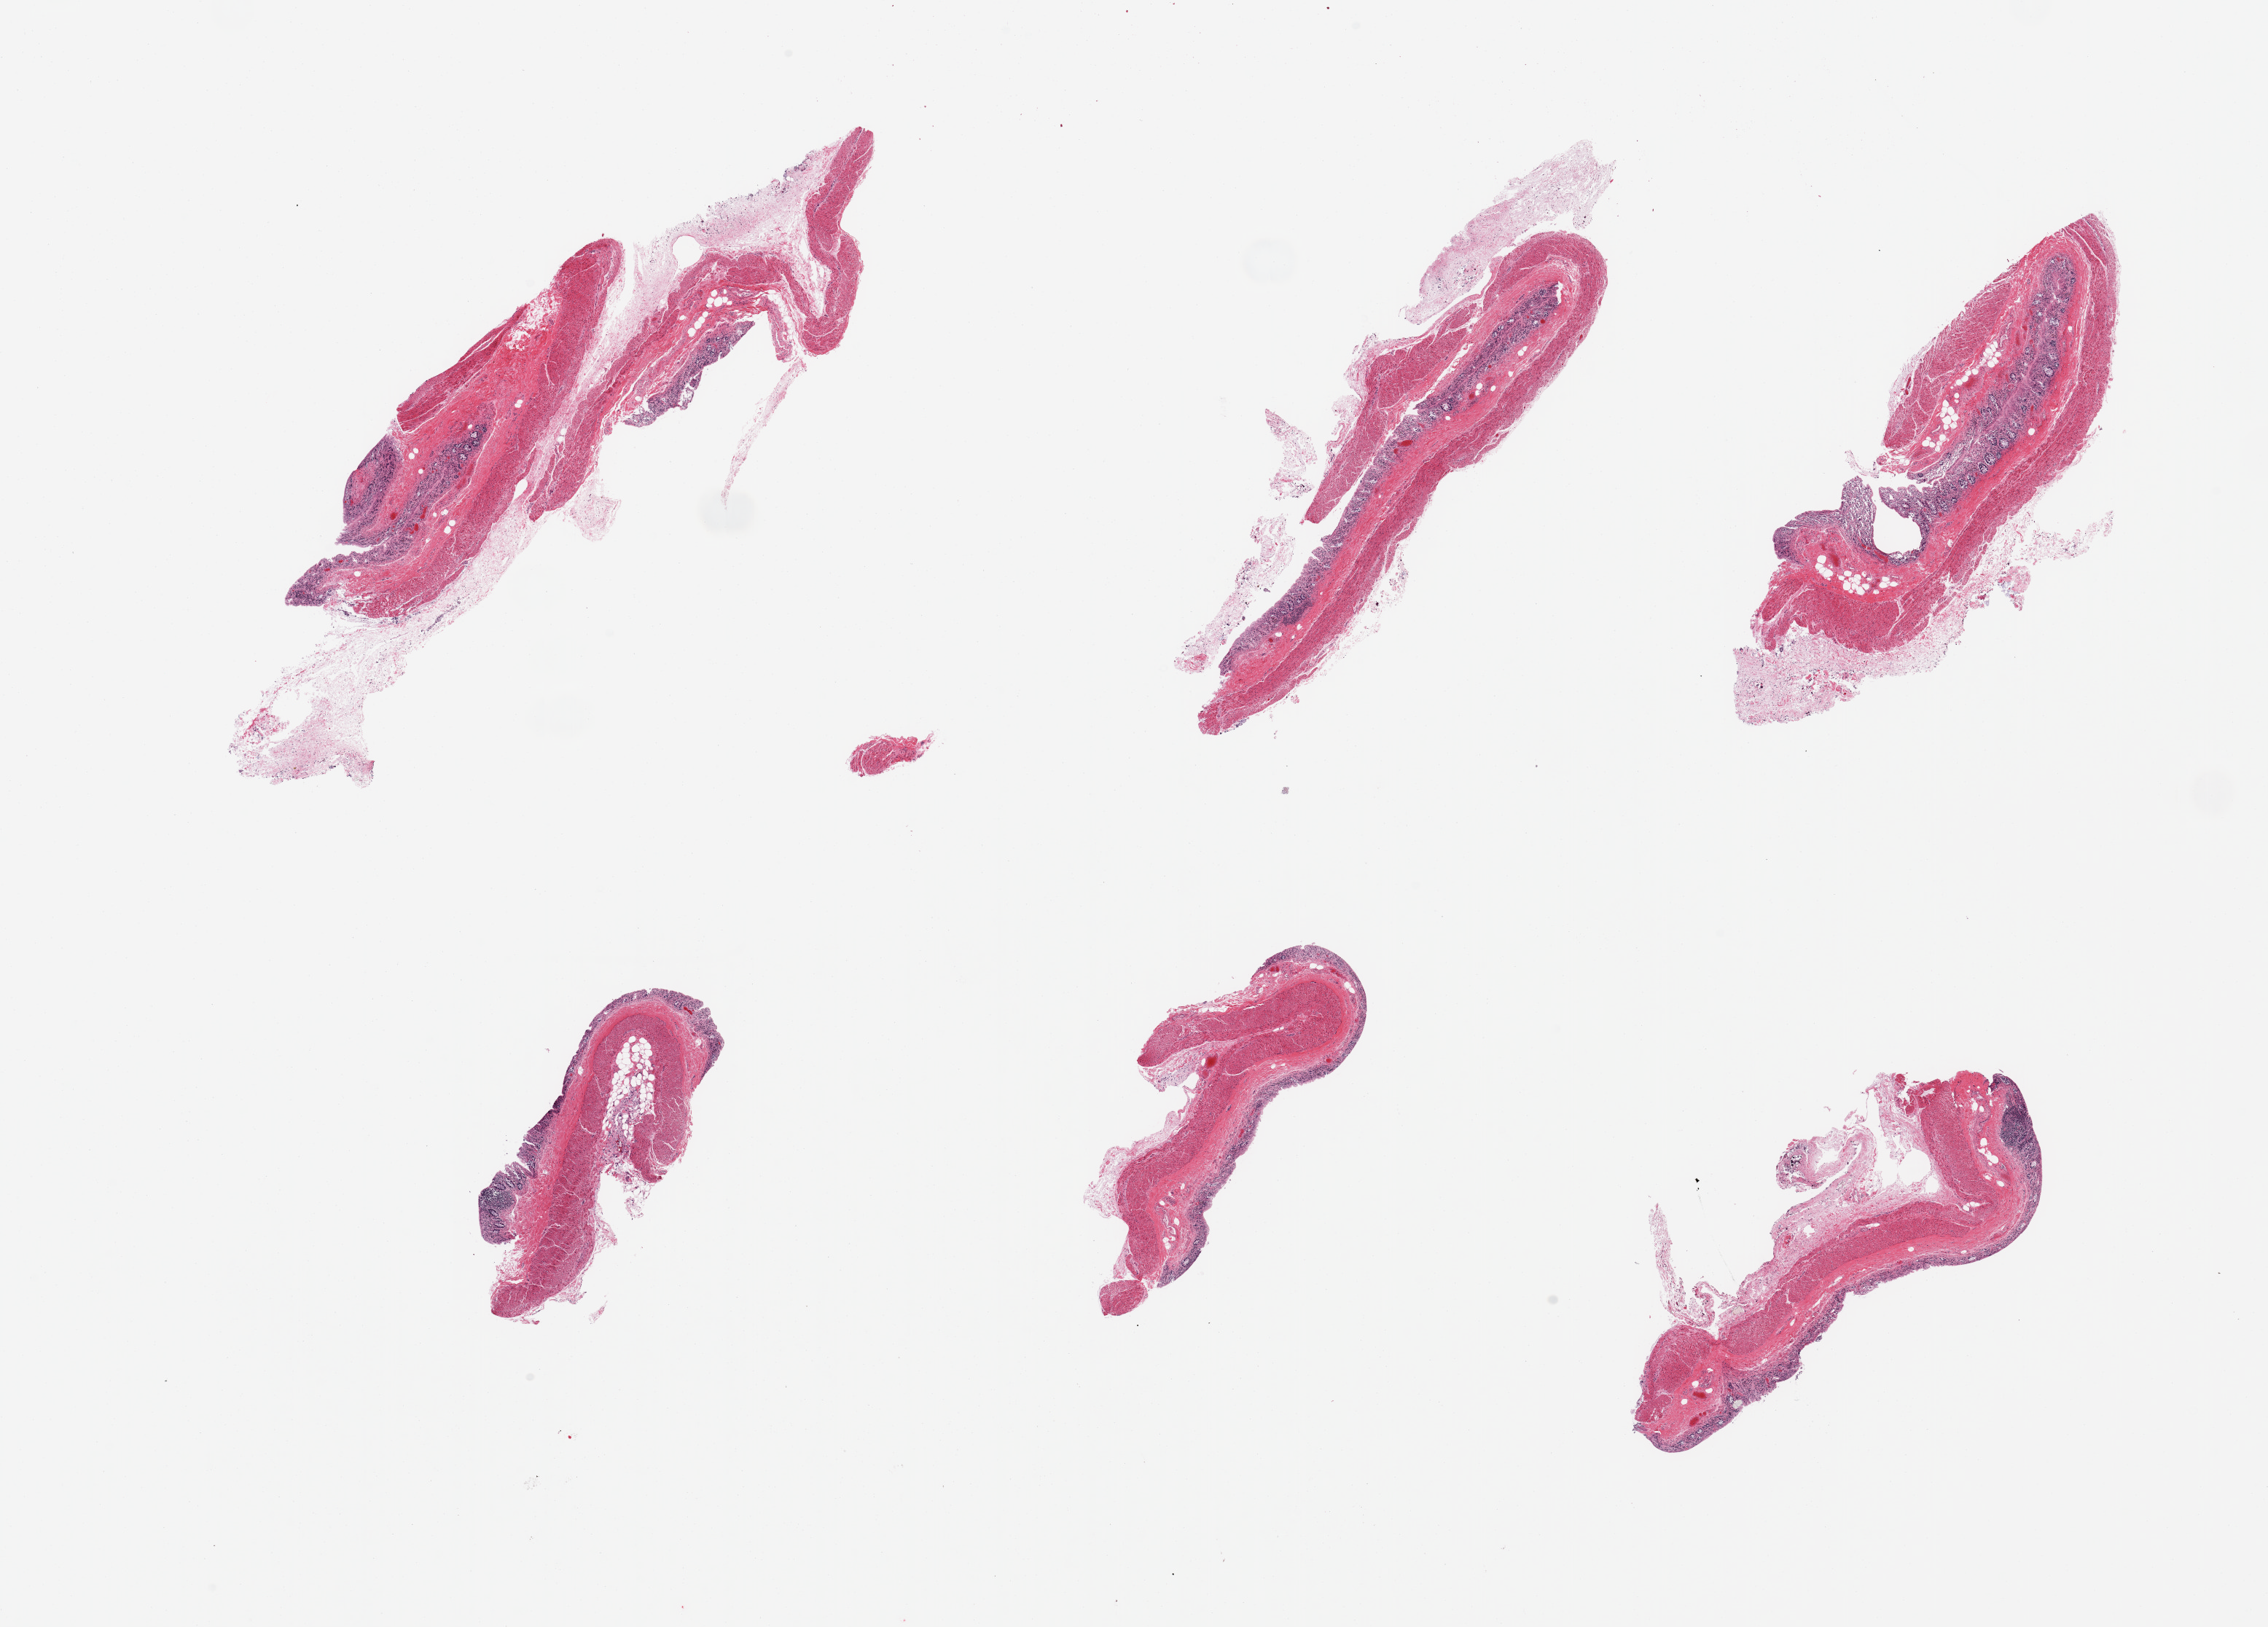
Whole-slide image, H&E stain — shown as a low-resolution overview of the whole scanned area (about 24.6 x 17.7 mm); PAXgene-fixed paraffin-embedded (PFPE) section; target tissue: transverse colon; tissue donor sample. Donor: female.
Pathologist's review note for this sample: 6 pieces; full thickness sections, mucosa largely autolyzed, some melanosis coli.